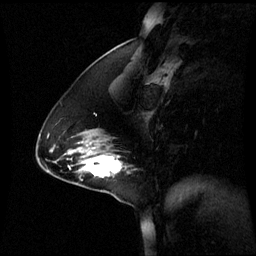
Breast MRI (dynamic contrast-enhanced), one sagittal slice; position 21 of 60 along the scan axis; dynamic contrast-enhanced series, image 2 of 3 at this slice position (ordered by acquisition); 1.5 T; TE 4.2 ms, TR 8.9 ms; 256 × 256 image matrix. Female patient, age 44 years. From the clinical record (not read from this slice): setting: breast cancer imaged before/during neoadjuvant chemotherapy; receptor status: triple-negative.
Outlined on this slice (semi-automatically segmented with operator editing):
- analysis volume of interest (the breast-tissue region the enhancement analysis was run in; not a lesion): bounding box [x1, y1, x2, y2] px = [76, 150, 129, 185]
- tumour enhancement mask (voxels above the 70 % enhancement threshold inside the analysis volume of interest): [82, 156, 121, 179]